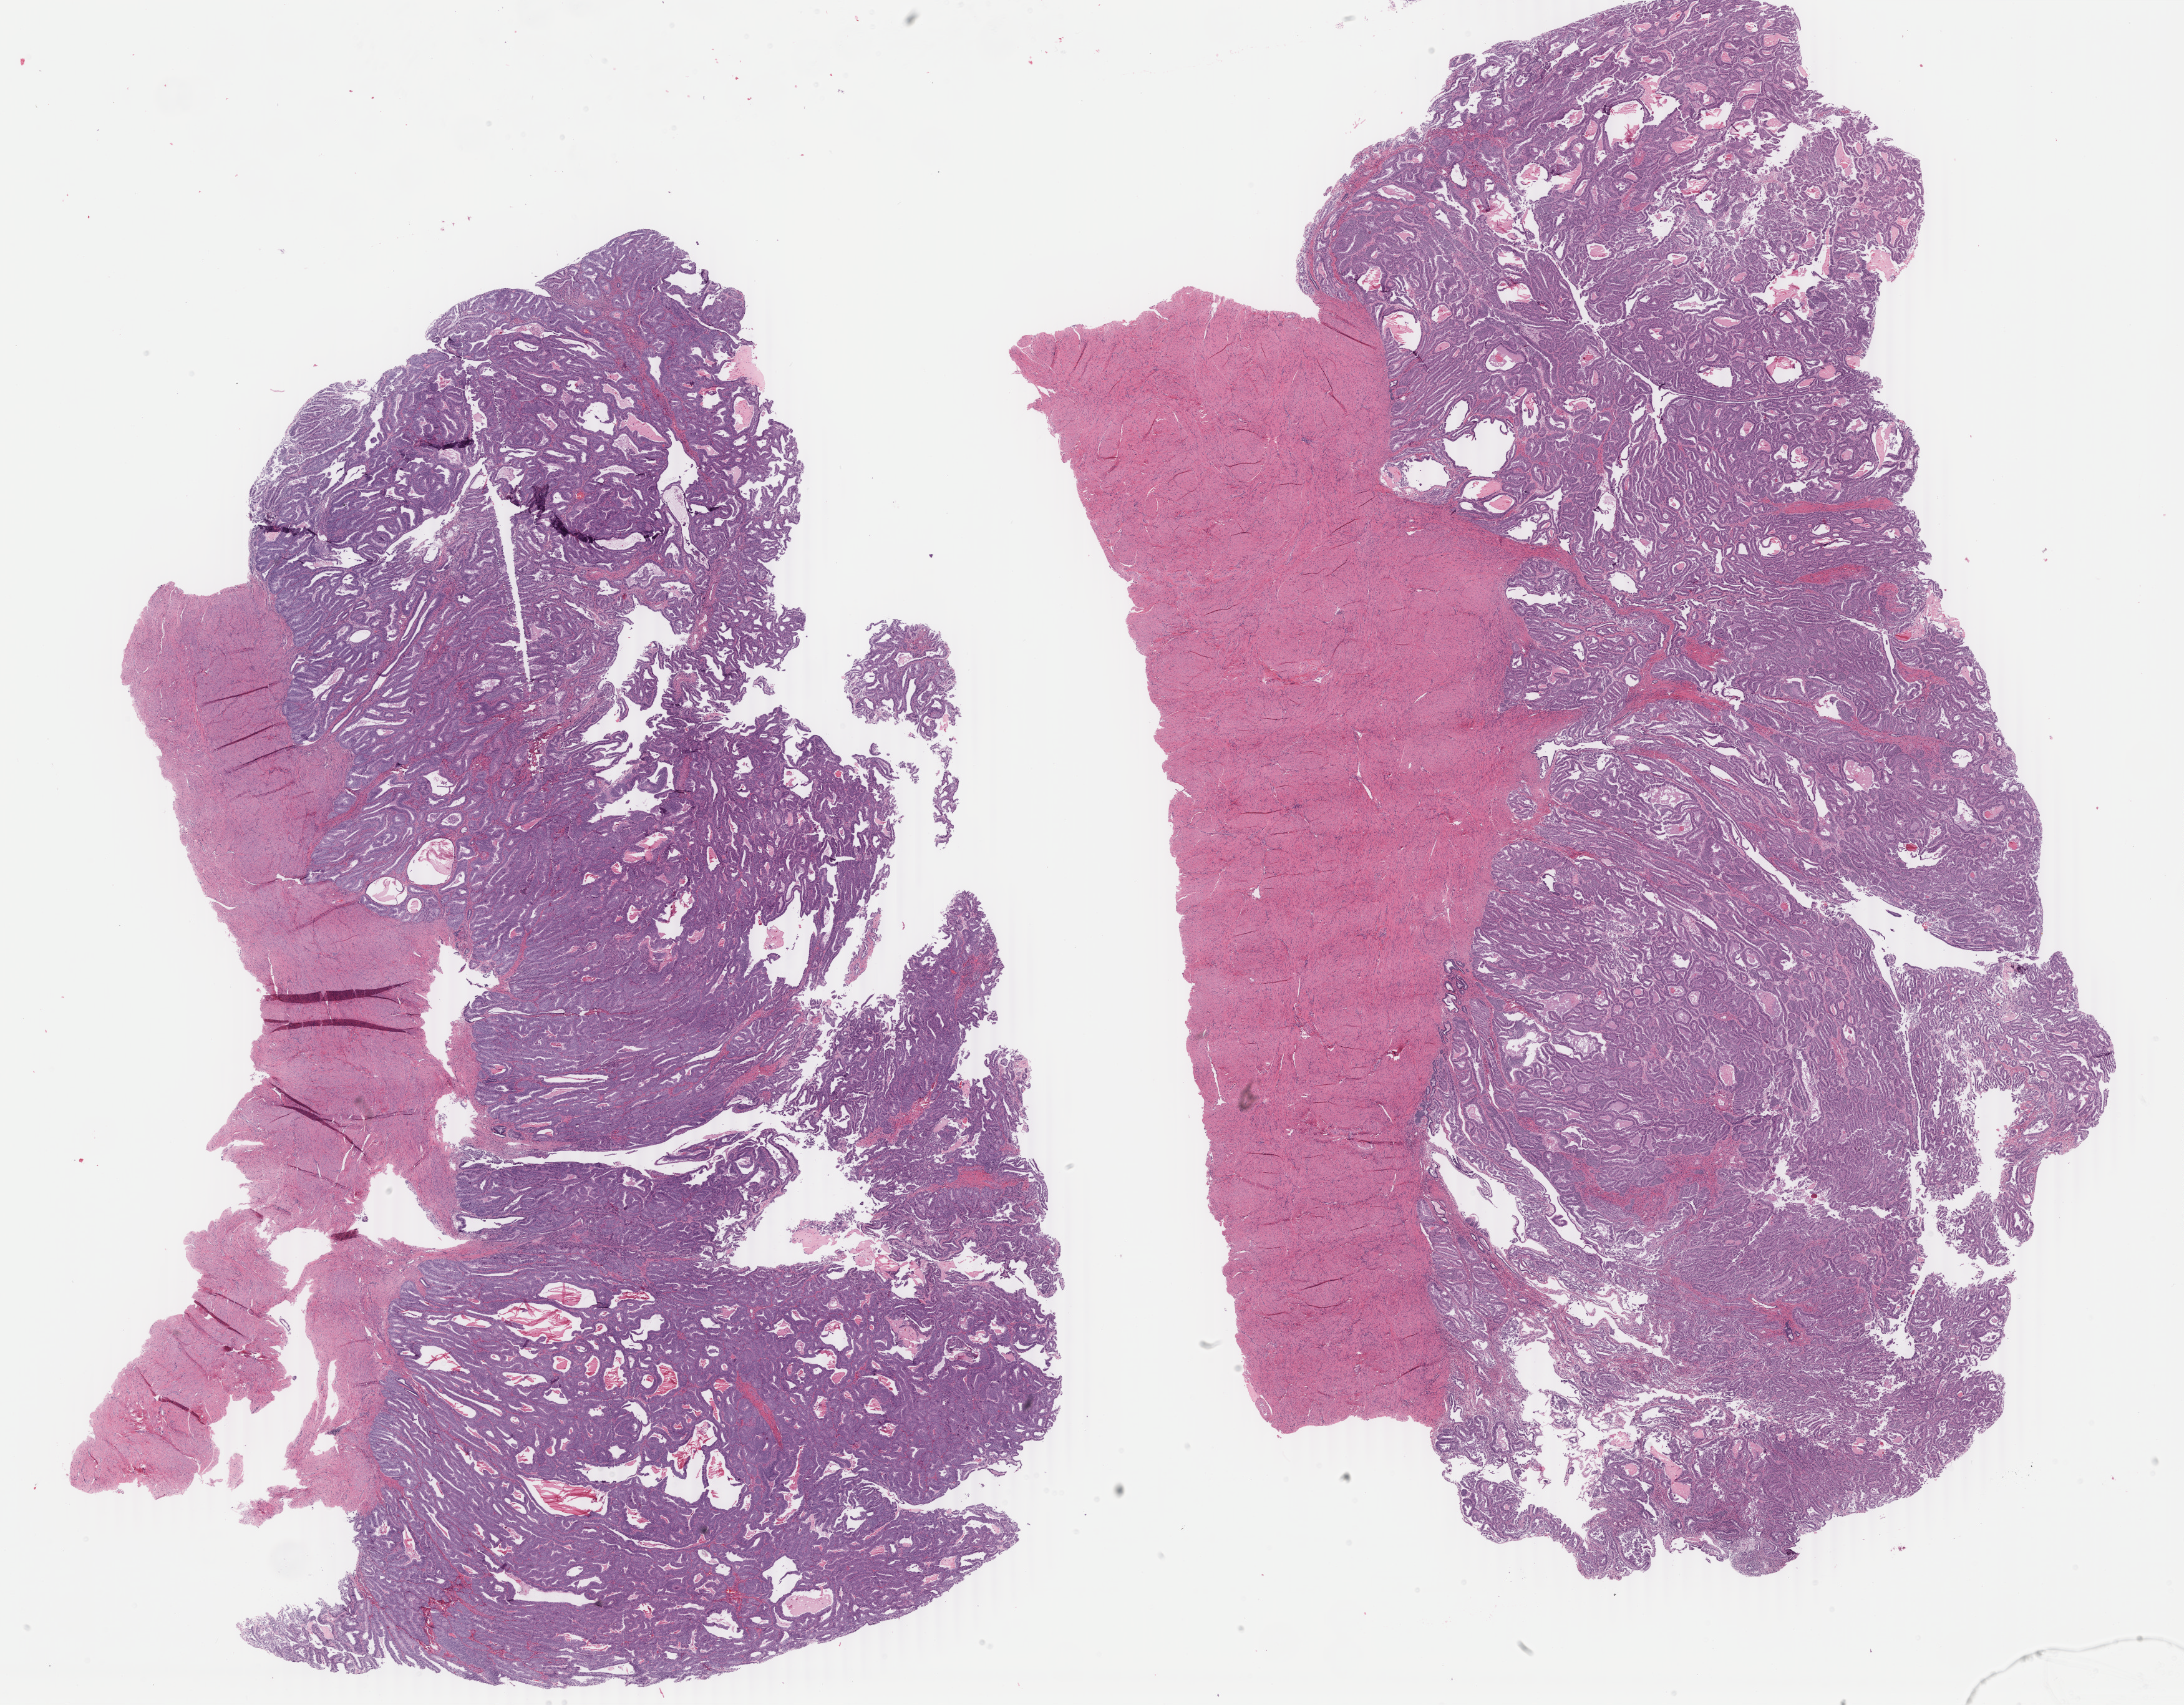
Whole-slide histology image, H&E-stained — a low-resolution overview of the entire scanned area, about 27.8 x 21.7 mm (acquisition: 40x scan), formalin-fixed paraffin-embedded (FFPE) diagnostic section, primary tumour sample from the uterus. Female patient; age at initial diagnosis 59 years.
Histologic diagnosis: Endometrioid adenocarcinoma, NOS (endometrium).